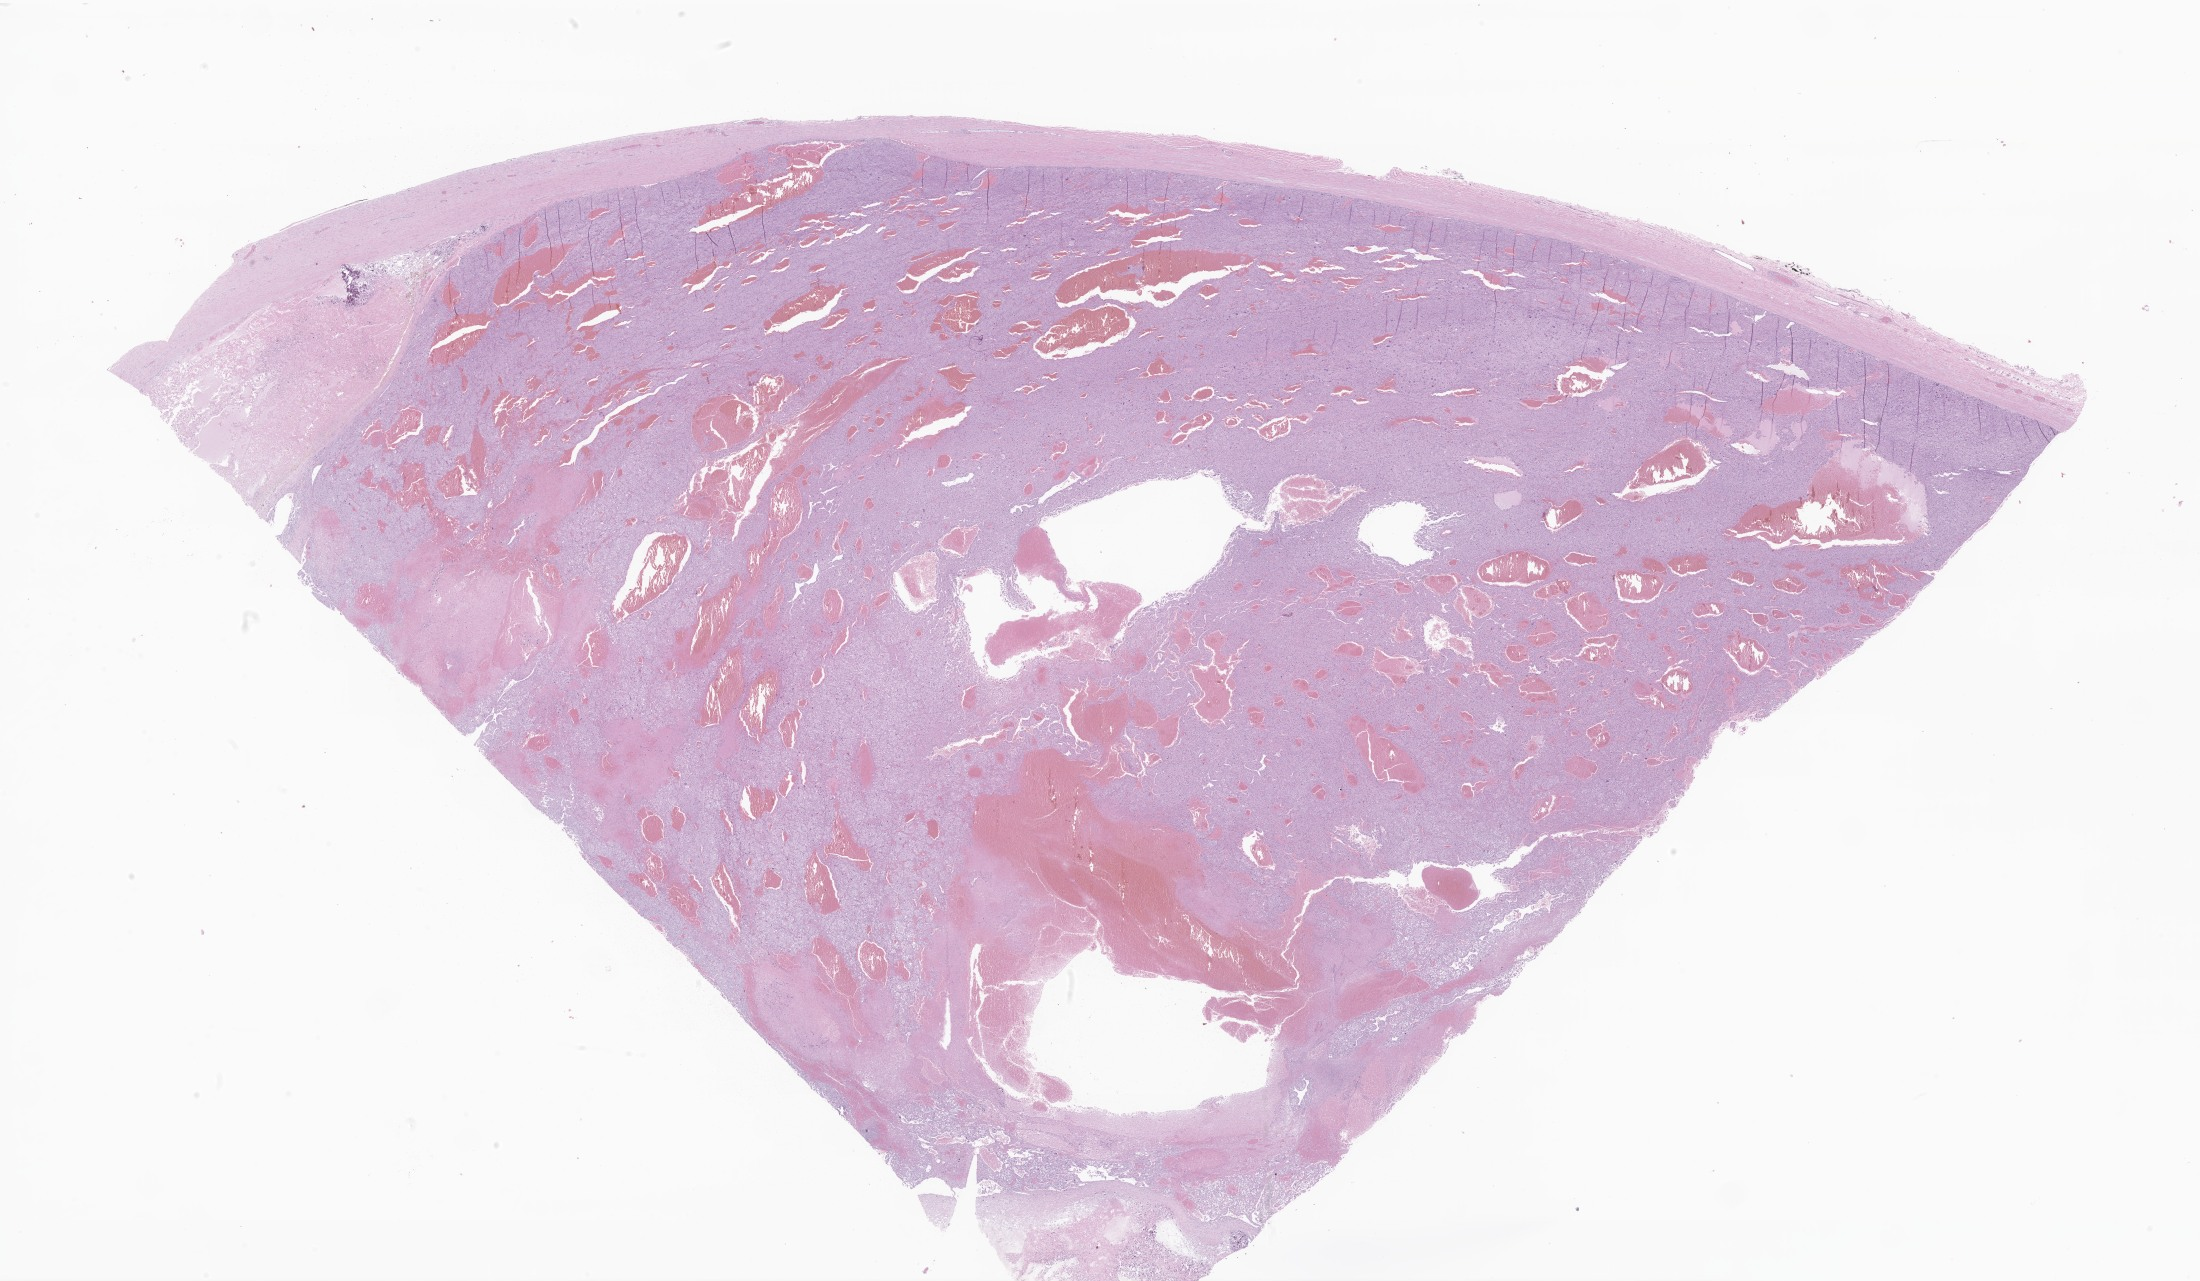
Whole-slide image, haematoxylin and eosin stain of tumor tissue from the adrenal gland — a low-resolution overview of the entire scanned area, about 37.1 x 21.6 mm. FFPE section. Patient: female, age 541 days (about 1.5 years).
Diagnosis (ICD-O-3 morphology term): Adrenal cortical carcinoma.